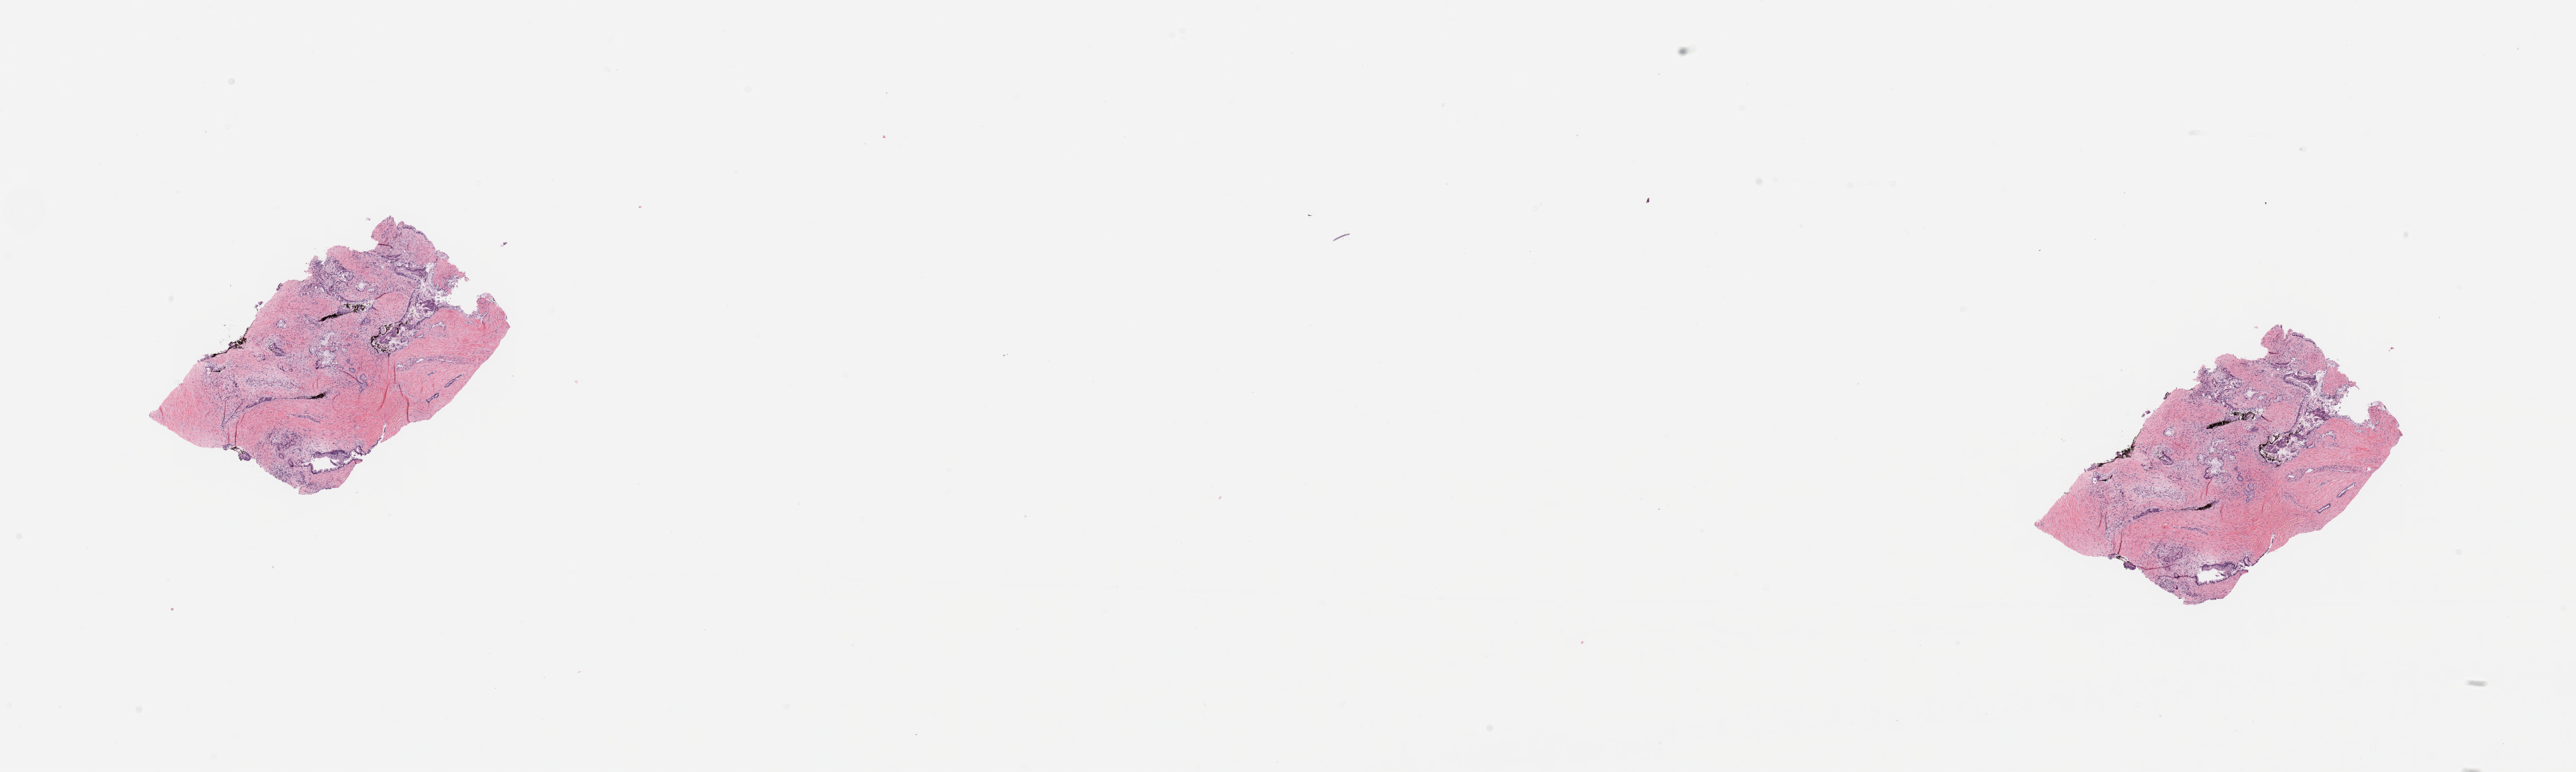
Whole-slide histology image, H&E — a low-resolution overview of the entire scanned area, about 29.5 x 8.9 mm. Pancreas, tumour tissue. Male, 67 y/o. Histologic grade: G2 (moderately differentiated).
• AJCC pathologic stage: IB
• diagnosis: Infiltrating duct carcinoma, NOS